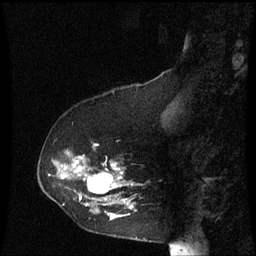
Breast MRI (dynamic contrast-enhanced), one sagittal slice; dynamic contrast-enhanced series, image 2 of 3 at this slice position (ordered by acquisition); 1.5 T; TE 4.2 ms, TR 8.9 ms; 2 mm slice thickness; 256 × 256 image matrix, field of view 200 × 200 mm. Female patient, age 53 years. Case-level facts recorded for this patient, not image findings: setting: breast cancer imaged before/during neoadjuvant chemotherapy; receptor status: HR-positive, HER2-negative.
Structures marked on this image (semi-automatically segmented with operator editing):
- analysis volume of interest (the breast-tissue region the enhancement analysis was run in; not a lesion): box from (x=38, y=144) to (x=141, y=221) px
- tumour enhancement mask (voxels above the 70 % enhancement threshold inside the analysis volume of interest): (x=62, y=144)–(x=133, y=219)